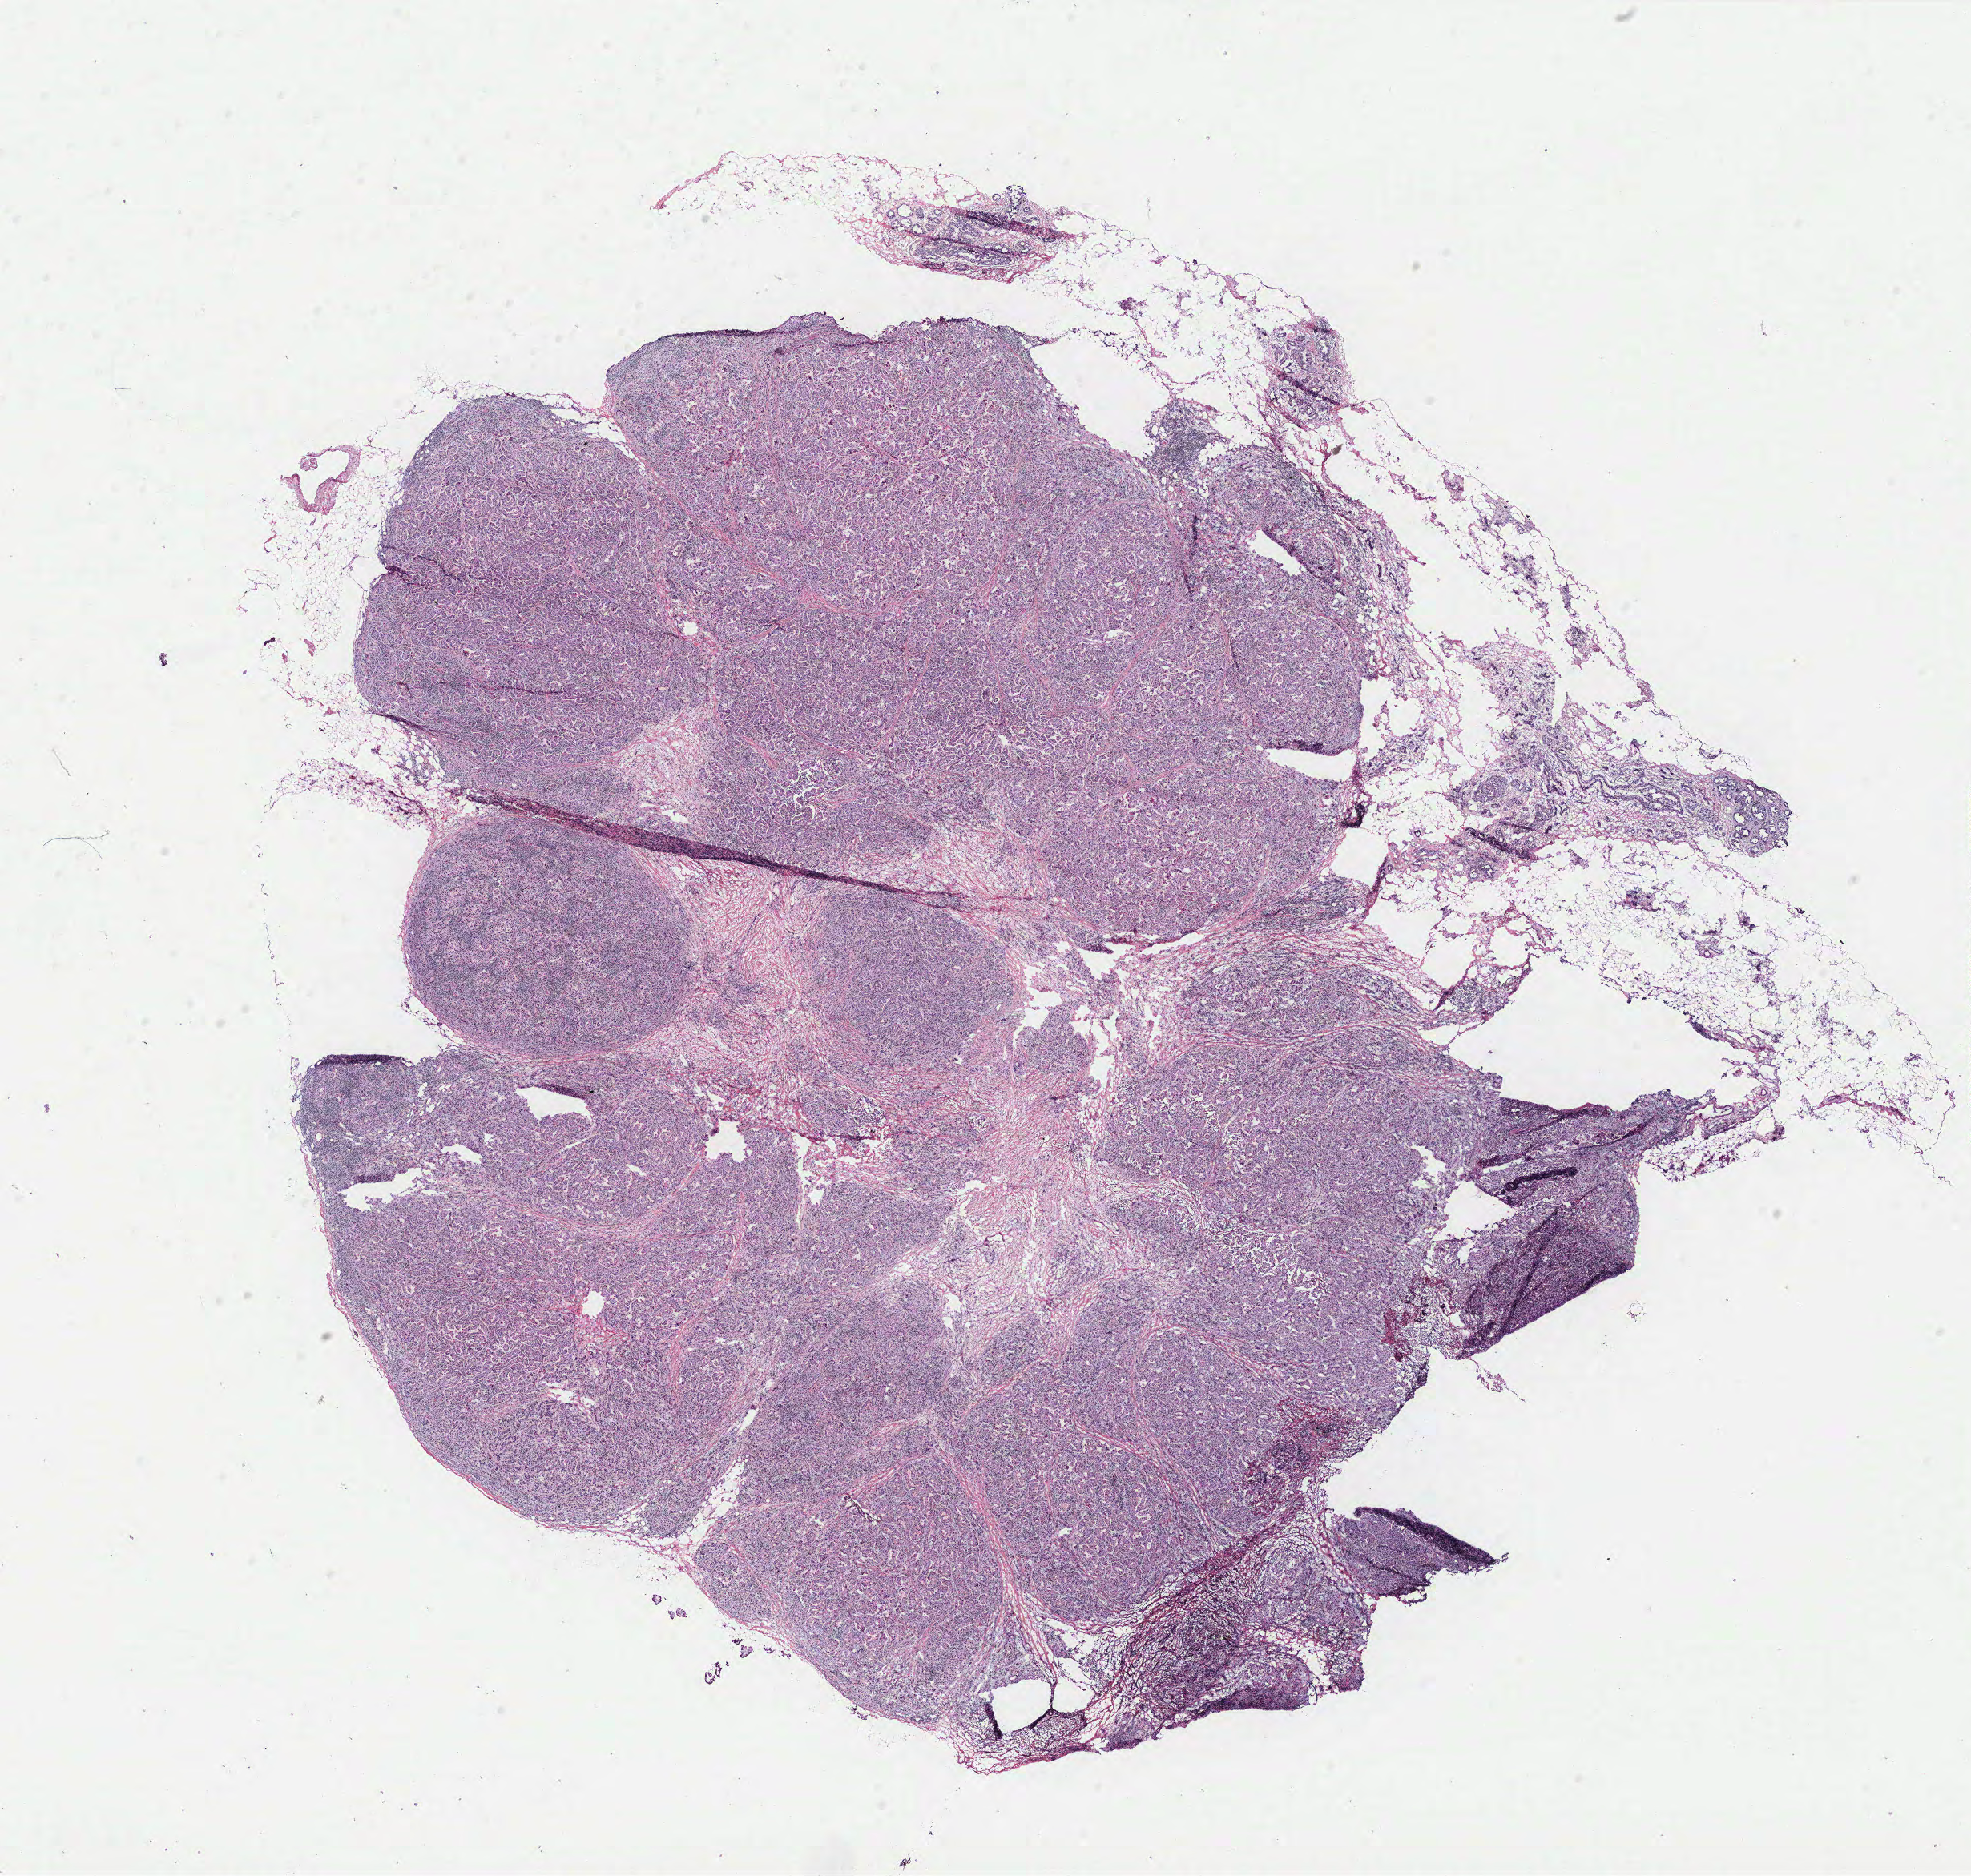
H&E whole-slide image — shown as a low-resolution overview of the whole scanned area (about 19.7 x 18.7 mm); breast, tissue type not recorded. Female, 71 y/o.
* patient diagnosis: Infiltrating duct carcinoma, NOS